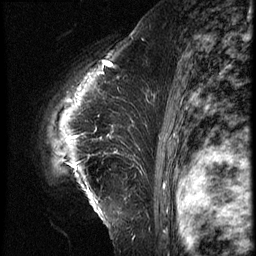
Breast MRI (dynamic contrast-enhanced), one sagittal slice. 3 images stored at this slice position (order not interpretable as contrast timing). 1.5 T. TE 4.2 ms, TR 9 ms. 2.5 mm slice thickness. 256 × 256 image matrix, field of view 180 × 180 mm. Female patient, age 39 years. From the clinical record (not read from this slice): setting: breast cancer imaged before/during neoadjuvant chemotherapy; receptor status: HER2-positive.
Annotated regions visible in this slice (semi-automatic segmentation, software-assisted and operator-edited):
- analysis volume of interest (the breast-tissue region the enhancement analysis was run in; not a lesion): box from (x=34, y=64) to (x=152, y=228) px
- tumour enhancement mask (voxels above the 140 % enhancement threshold inside the analysis volume of interest): (x=77, y=64)–(x=113, y=138)